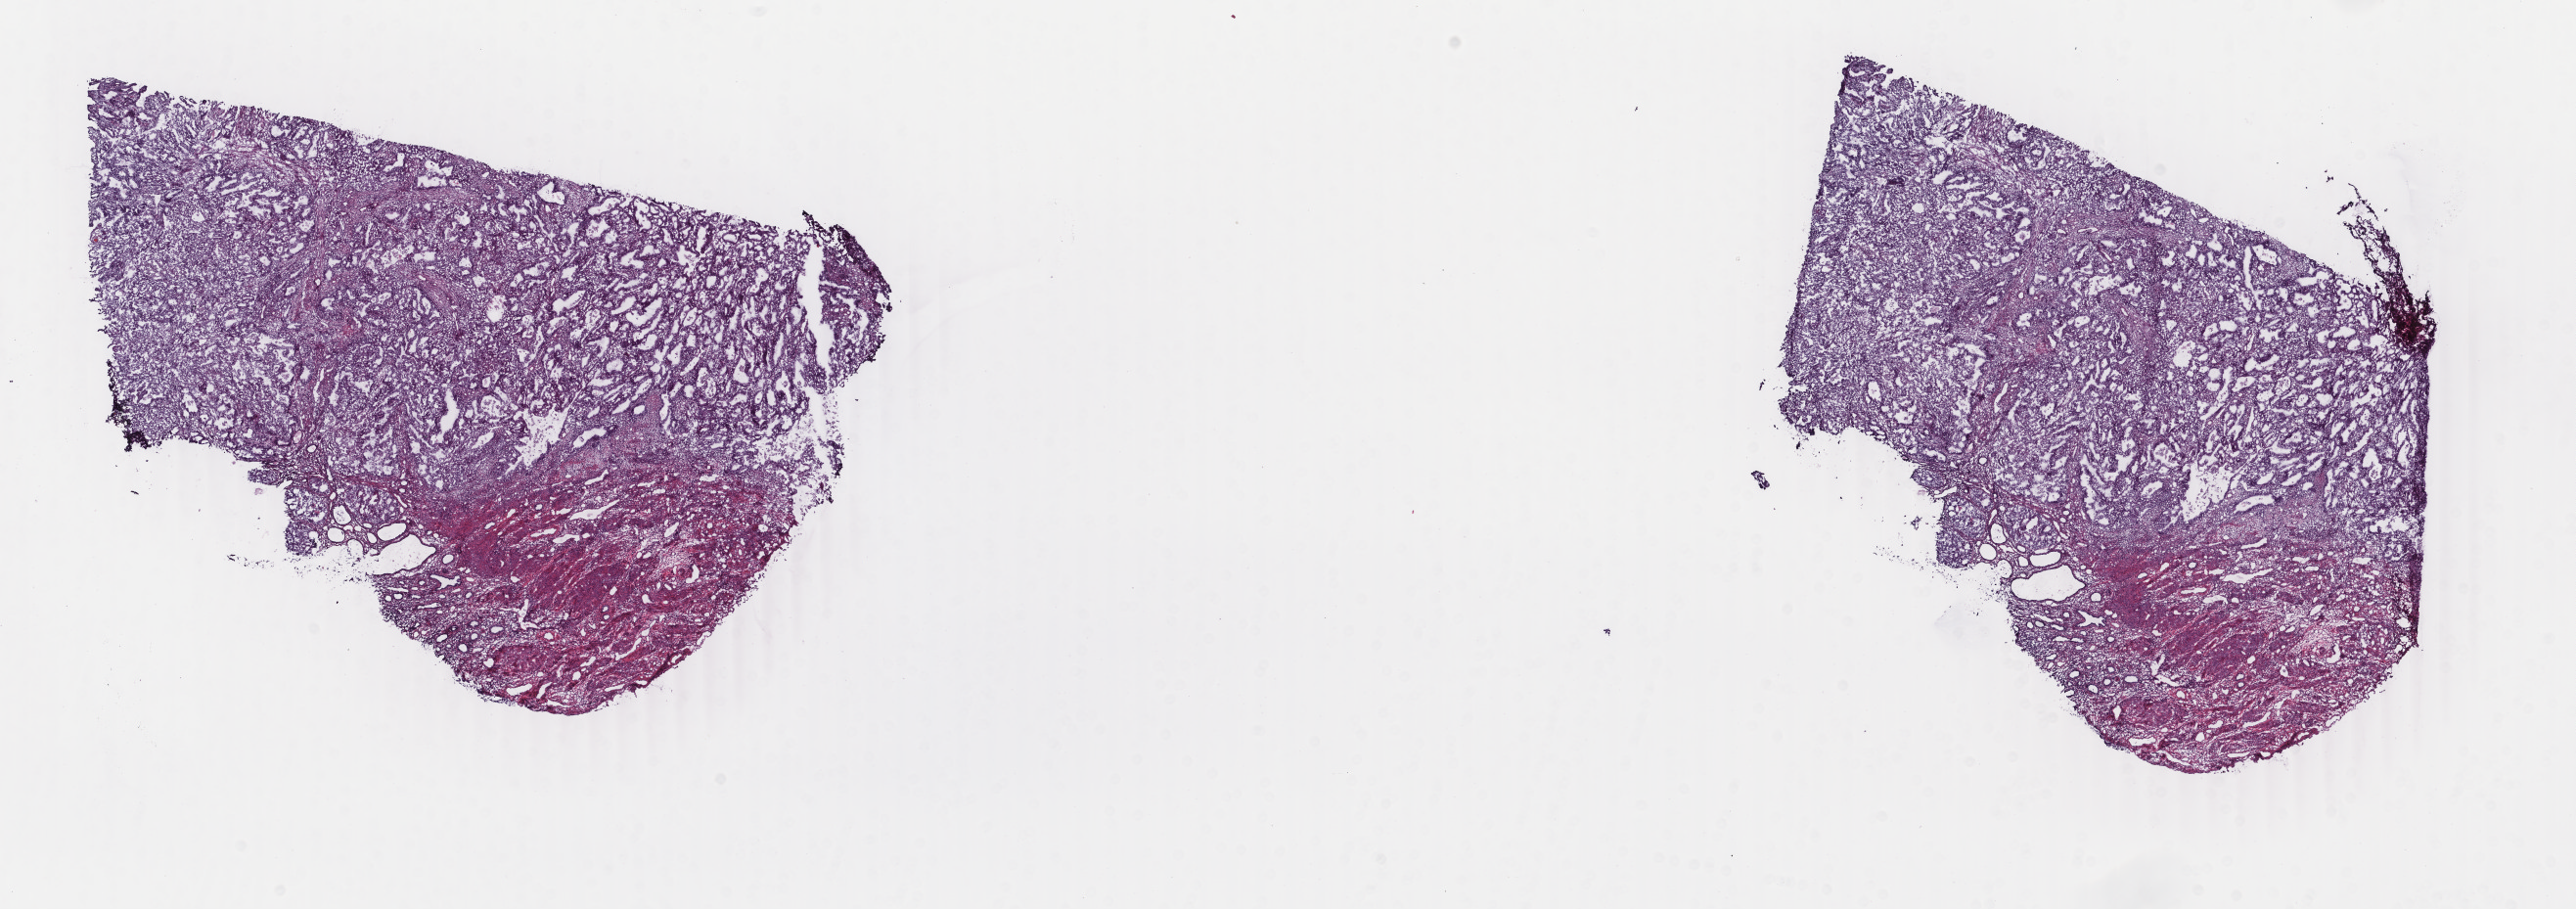
Digitized Hematoxylin and eosin (H&E) stained tissue section (whole slide), shown as a low-resolution overview of the whole scanned area (about 20.9 x 7.4 mm). Frozen section from the top of the tissue portion. Primary tumour sample from the uterus. Patient: female, age at initial diagnosis 78 years.
Histologic diagnosis: Endometrioid adenocarcinoma, NOS (endometrium).